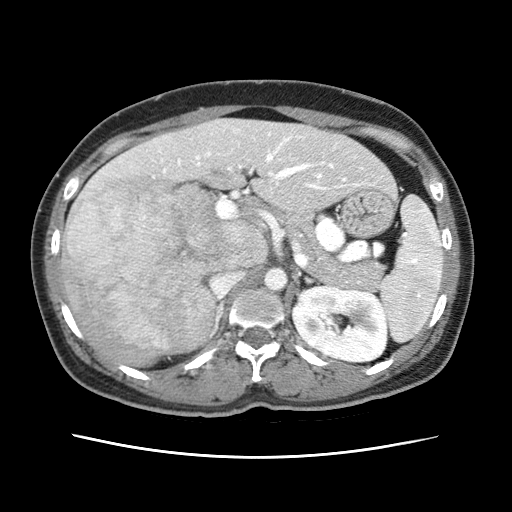
Contrast-enhanced abdominal CT (liver protocol), one axial slice; position 32 of 79 along the scan axis; reconstruction kernel STANDARD; 120 kVp; soft-tissue window (W 400 / L 40 HU); 512 × 512 image matrix, field of view 340 × 340 mm. Case-level facts recorded for this patient, not image findings: diagnosis: hepatocellular carcinoma (patient treated with transarterial chemoembolisation; whether this scan precedes or follows treatment is not stated here); TNM stage (as recorded): Stage-I; Child-Pugh class: A; tumour differentiation: moderately differentiated; tumour nodularity: uninodular.
Structures marked on this image (semi-automatically segmented with operator editing):
- abdominal aorta: bounding box (x1, y1, x2, y2) in pixels: (264, 268, 286, 290)
- liver parenchyma outside the tumour (the mass and vessels are separate outlines, so this box may not span the whole liver): (60, 118, 392, 364)
- mass: (61, 175, 230, 362)
- liver vessels: (153, 130, 363, 190)